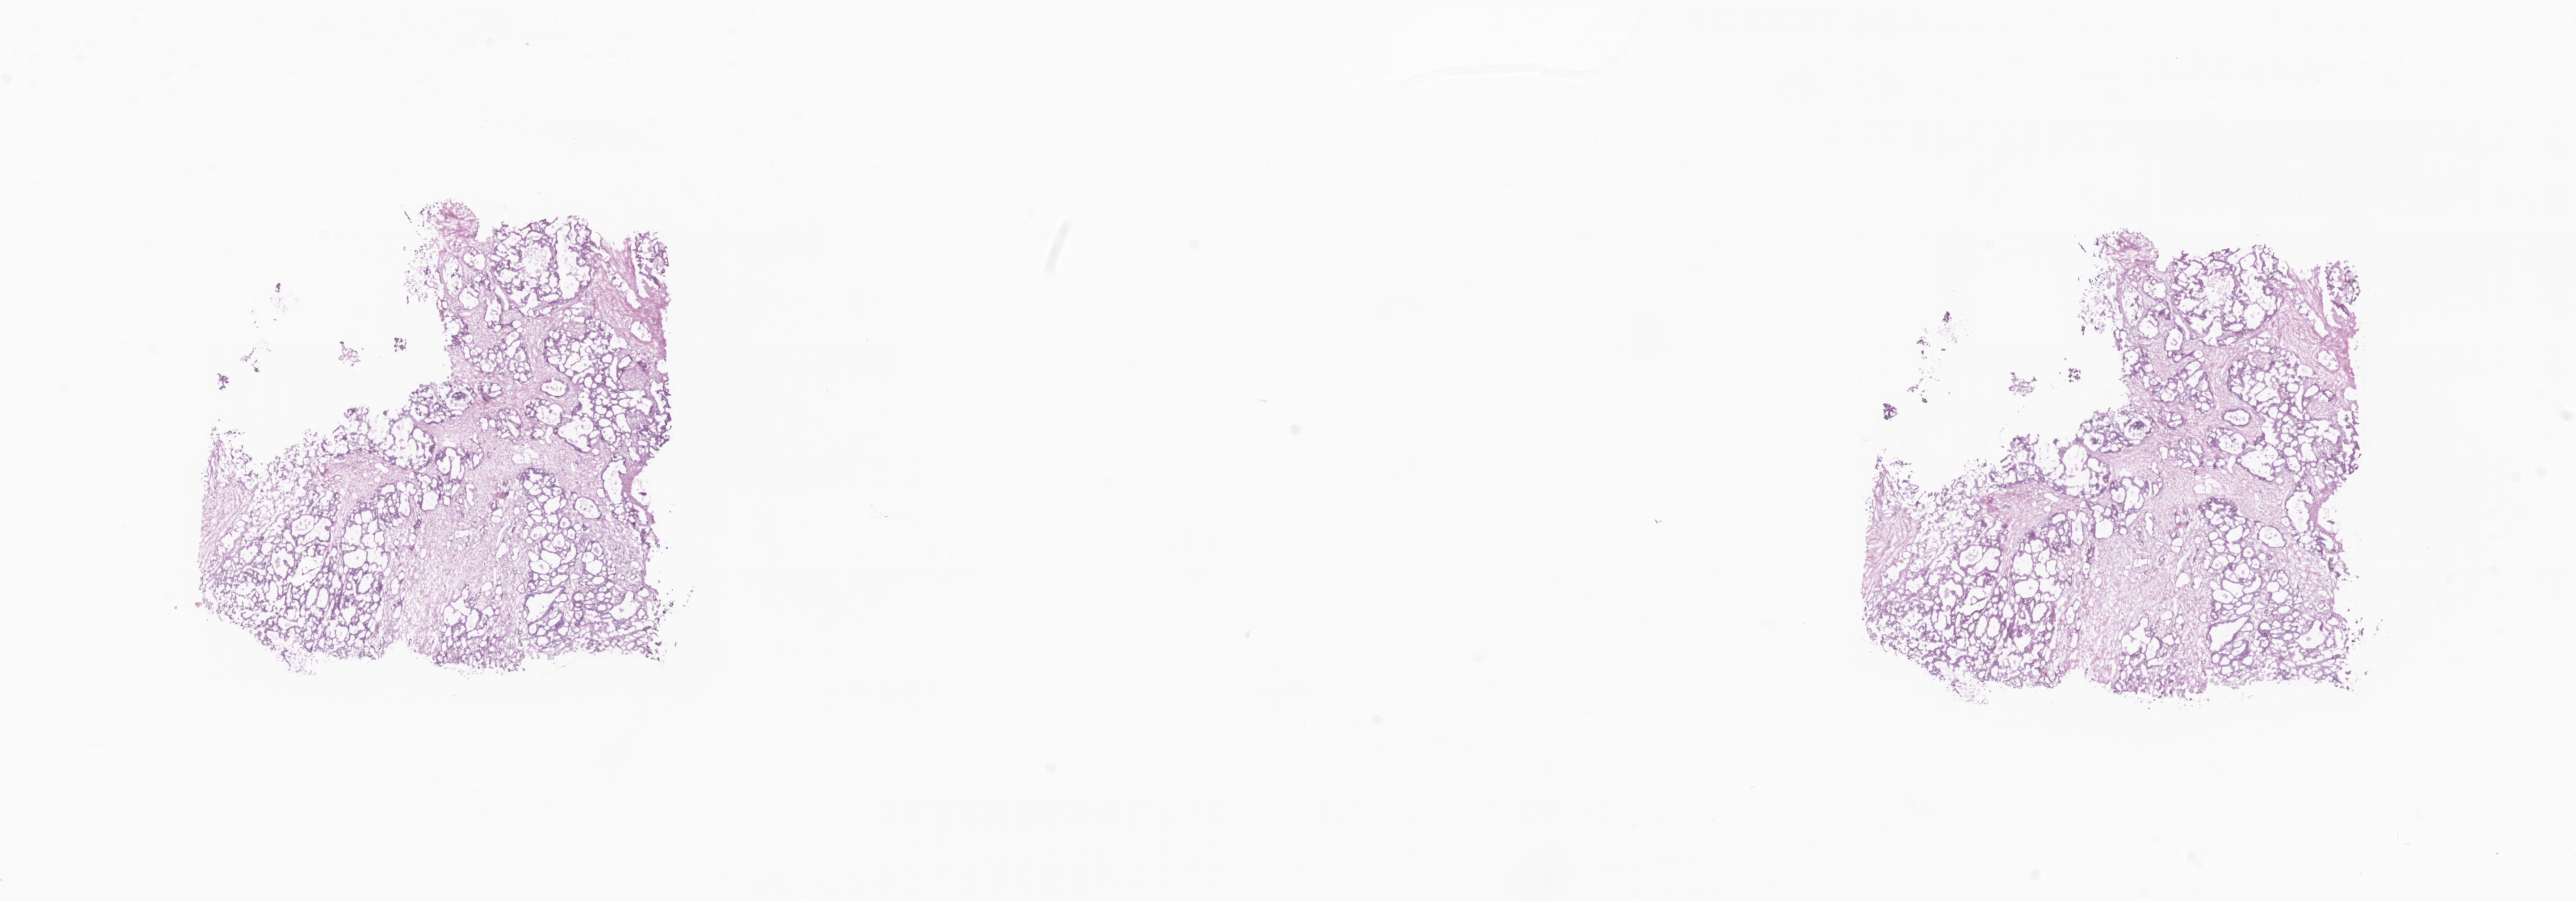
Whole-slide image, haematoxylin and eosin stain — a low-resolution overview of the entire scanned area, about 24.3 x 8.5 mm; cryosection; specimen: metastatic tumor tissue, resected from liver. Male, age 66 years at initial diagnosis. Composition of this section per pathologist review: tumor cells 80%, tumor nuclei 80%.
Patient diagnosis (primary): Adenocarcinoma, NOS.